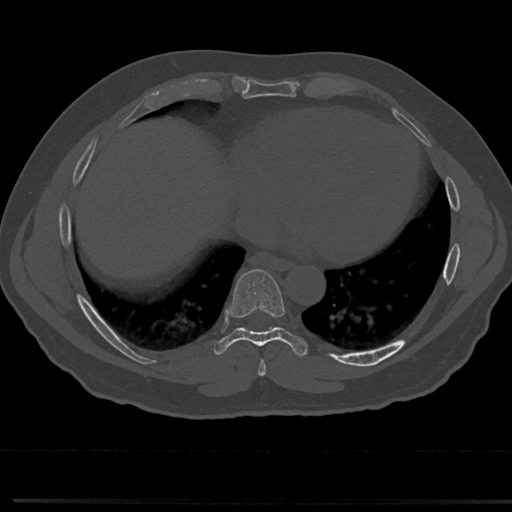
CT including the spine, one axial slice; 120 kVp; bone window (W 1800 / L 400 HU); 0.5 mm slice thickness; 512 × 512 image matrix, field of view 355 × 355 mm. Patient: male, 61 years. Case-level facts recorded for this patient, not image findings: primary cancer: prostate.
Annotated regions visible in this slice (semi-automatically segmented with operator editing):
- T7 vertebra: box from (x=241, y=330) to (x=282, y=363) px
- T8 vertebra: (x=236, y=270)–(x=284, y=335)